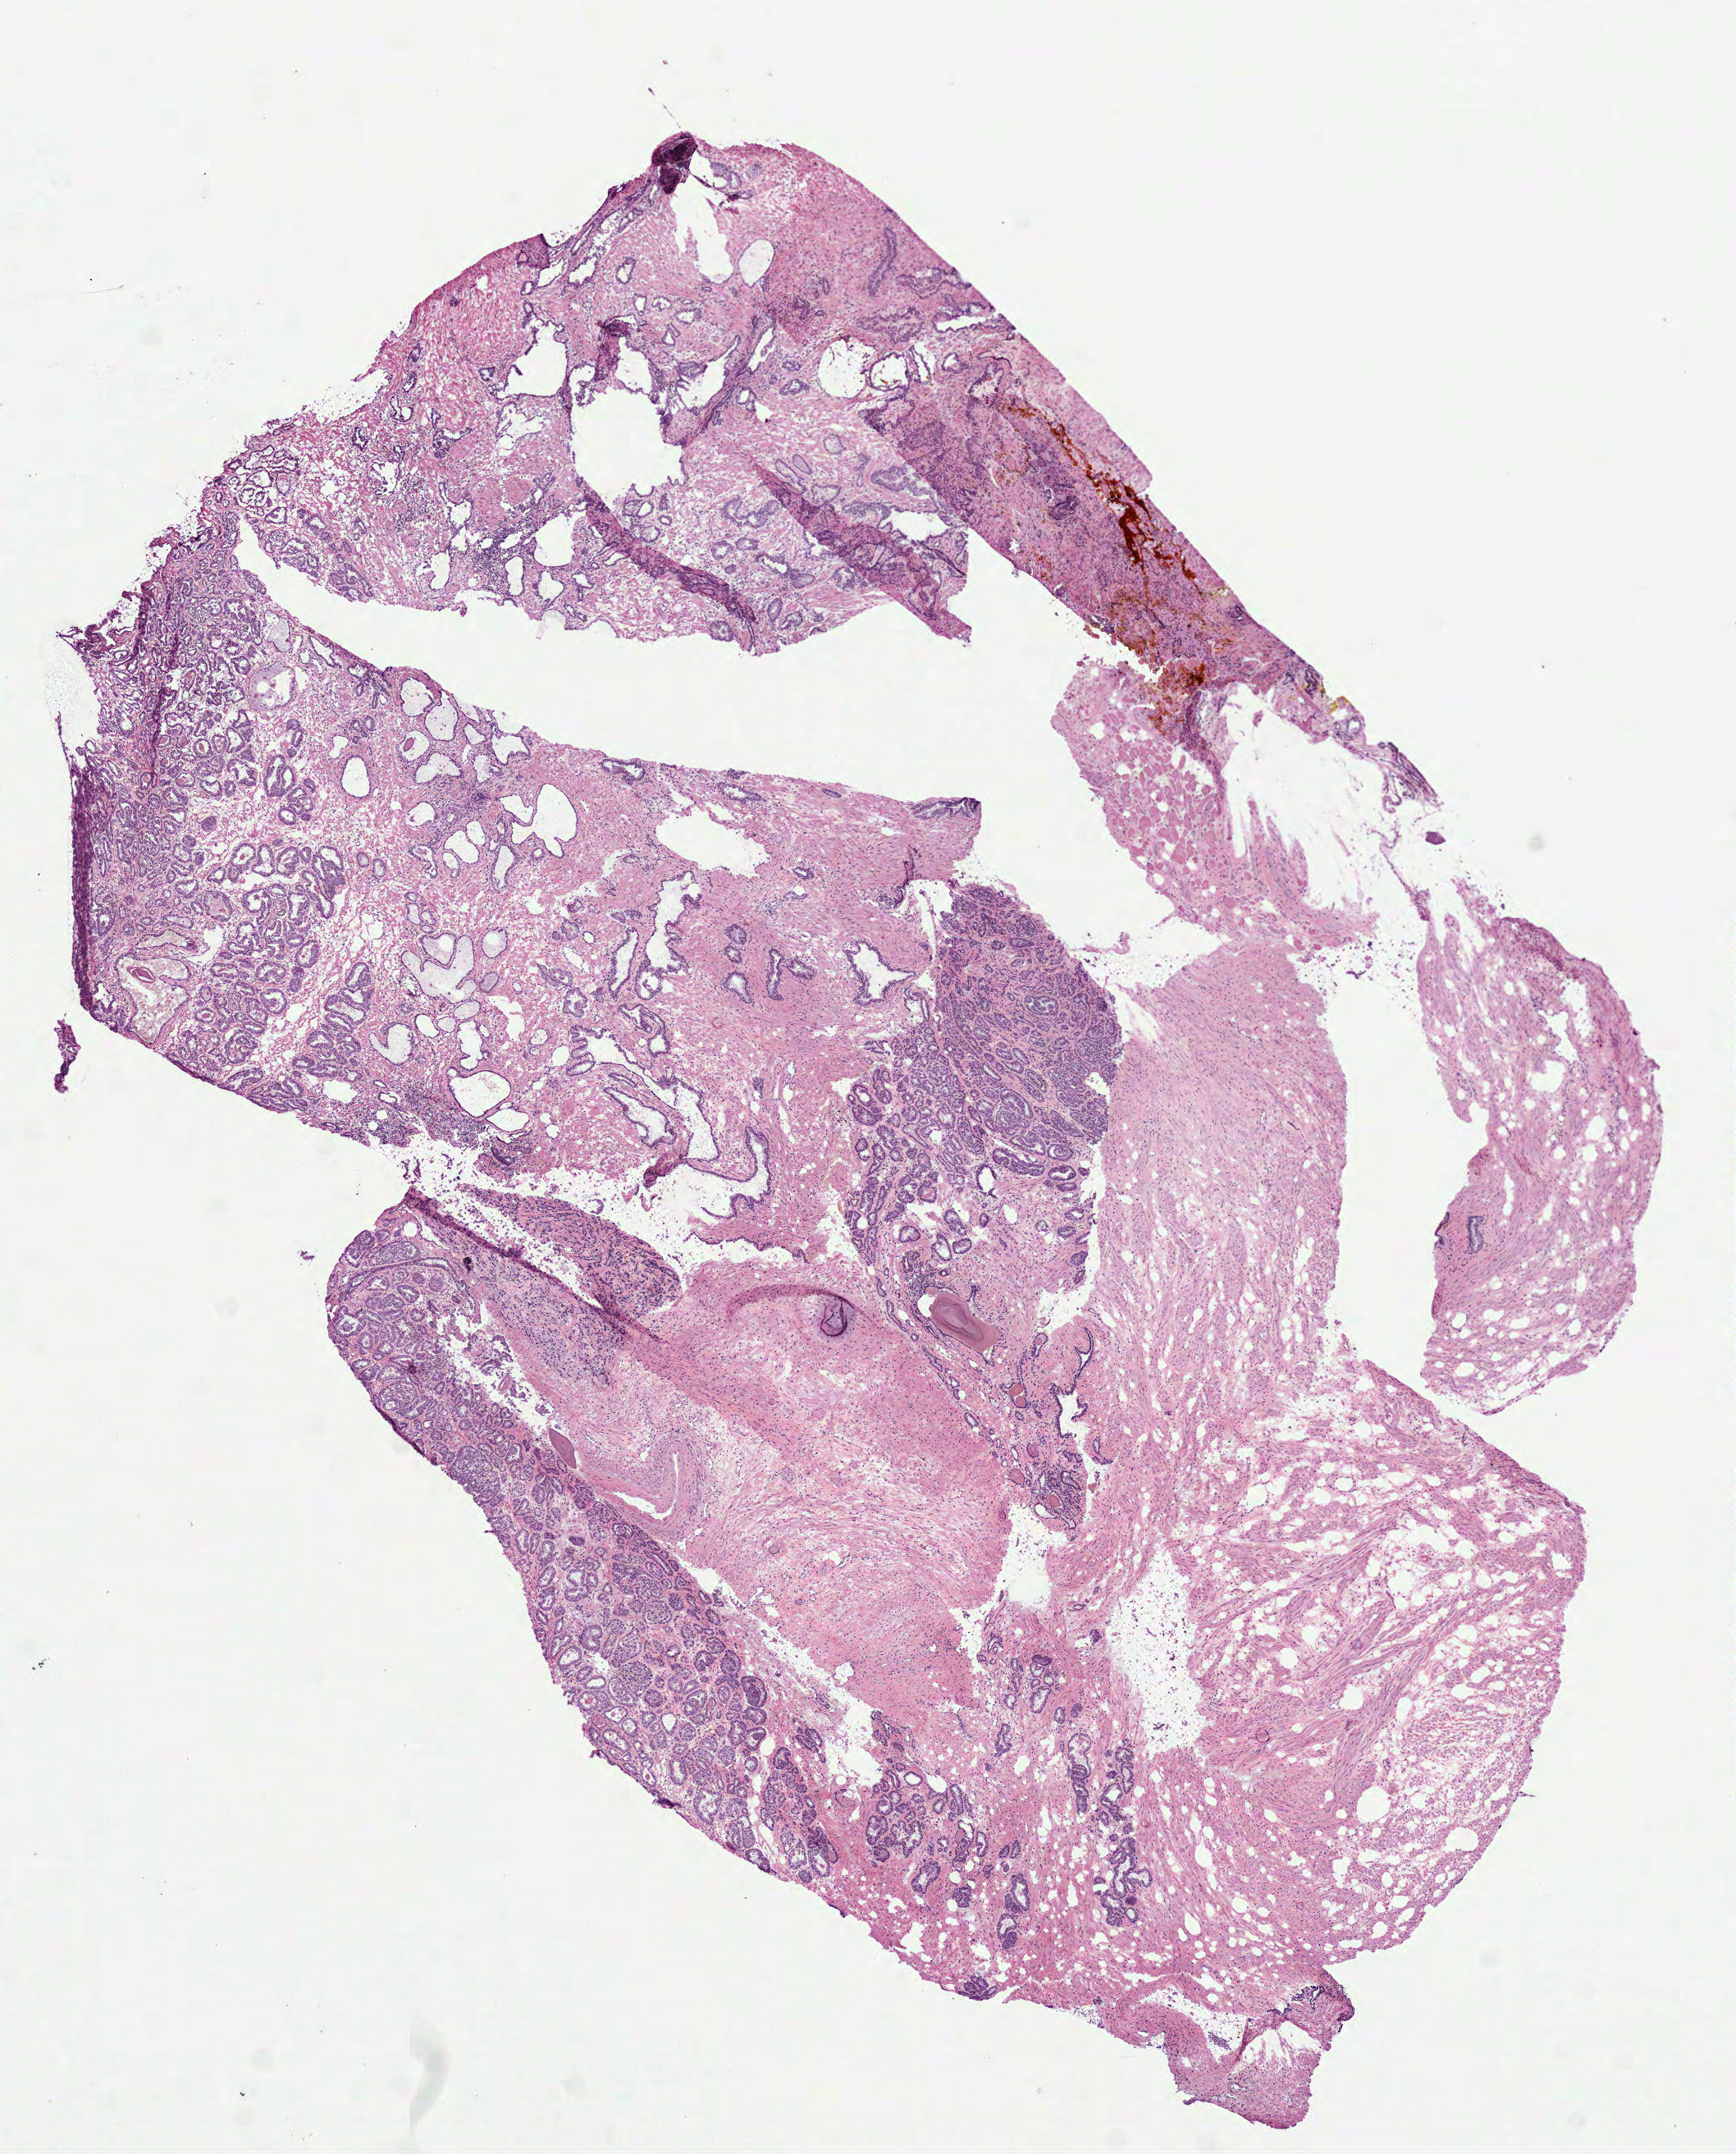
Whole-slide histology image, Hematoxylin and eosin (H&E) stained — a low-resolution overview of the entire scanned area, about 8.5 x 10.6 mm. Frozen section from the top of the tissue portion. Prostate, solid tissue normal (non-tumour tissue) sample. Male patient; age at initial diagnosis 66 years.
• this section: solid tissue normal sample (biorepository sample class)
• patient diagnosis: Acinar cell carcinoma (prostate gland)